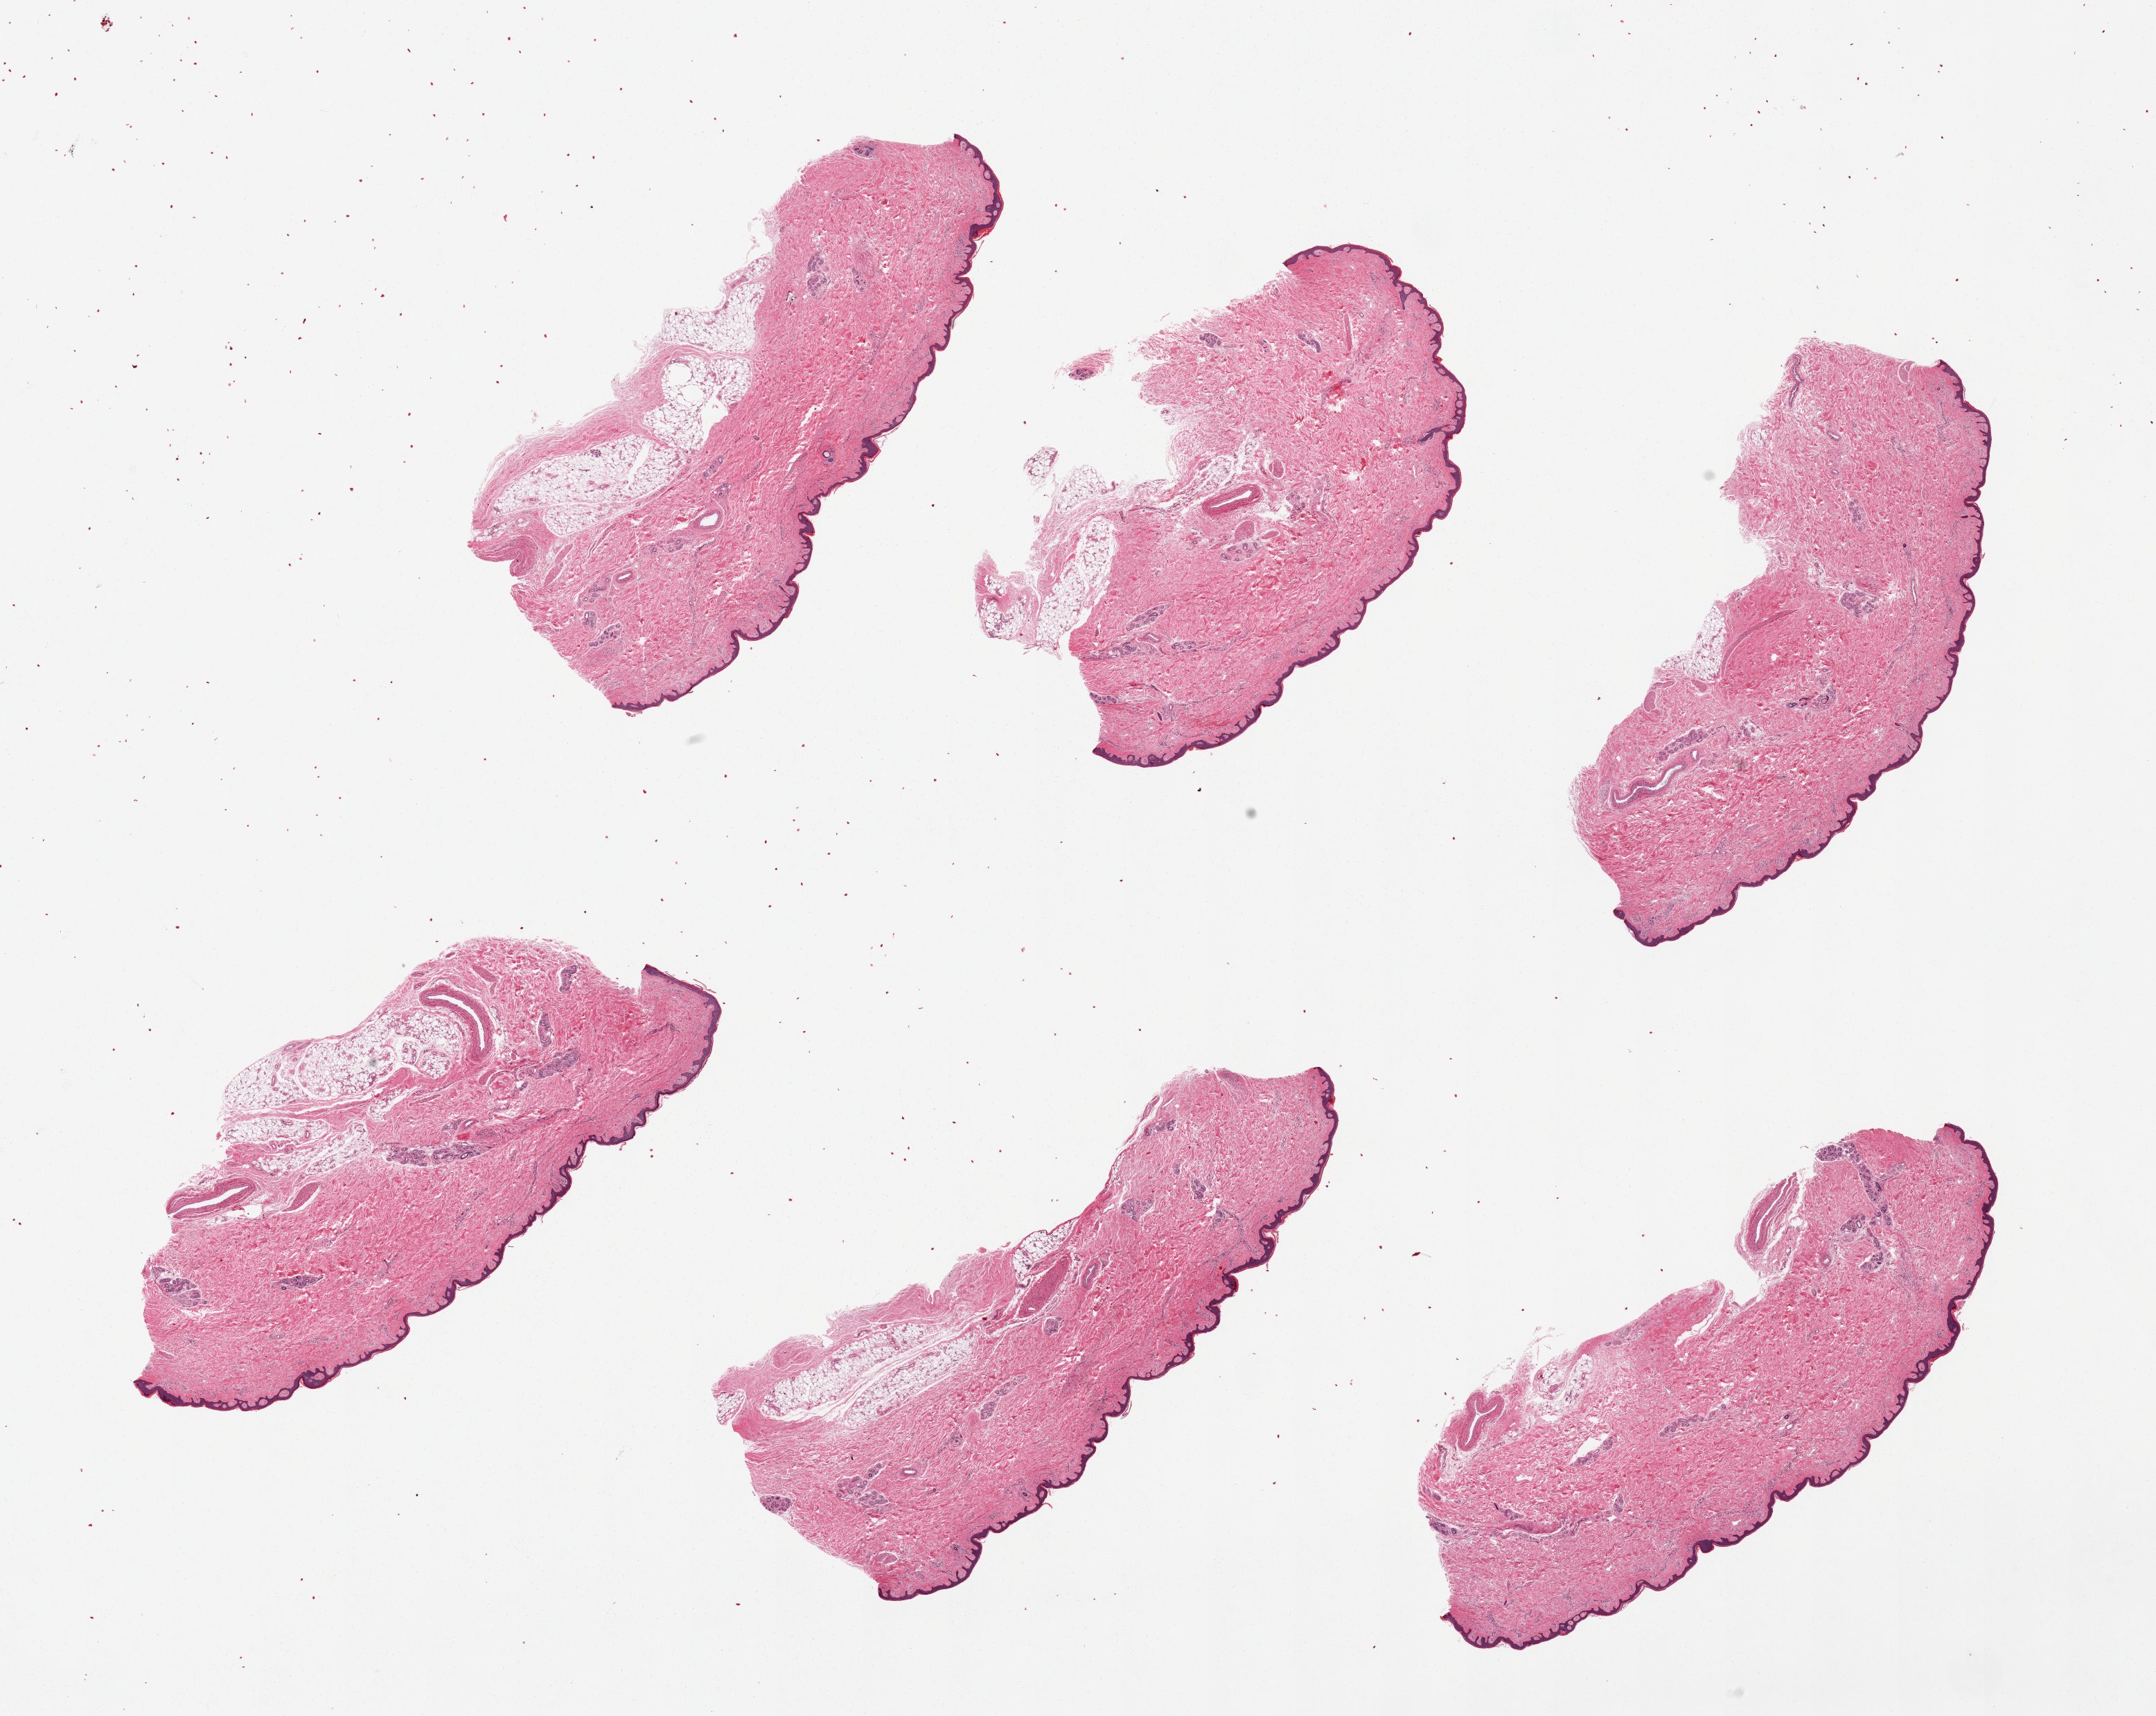
Hematoxylin and eosin (H&E) whole-slide image — whole scanned area (about 24.6 x 19.6 mm) shown as a low-resolution overview, PAXgene-fixed, paraffin-embedded tissue, target tissue: skin of lower leg, tissue donor sample. Male donor.
Pathologist's review note for this sample: 6 pieces; residual adipose tissue comprises ~5-10%; squamous epithelium is 1.5-3% of thickness.